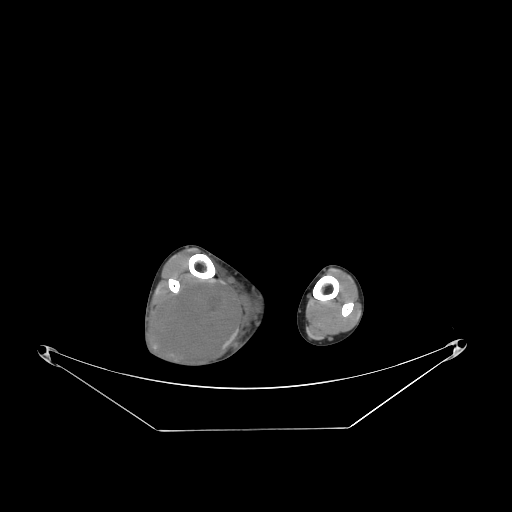
CT of an extremity soft-tissue mass (from a PET/CT study), one axial slice; soft-tissue window (W 400 / L 40 HU); 3.75 mm slice thickness; 512 × 512 image matrix, field of view 500 × 500 mm. Male patient. Case-level facts recorded for this patient, not image findings: histological type: liposarcoma - round cell; grade: high; site of the primary tumour: right calf.
Annotated regions visible in this slice (expert contour drawn on MRI and transferred to this co-registered scan by the dataset authors):
- gross tumour volume (mass): bounding box (x1, y1, x2, y2) in pixels: (153, 276, 266, 368)